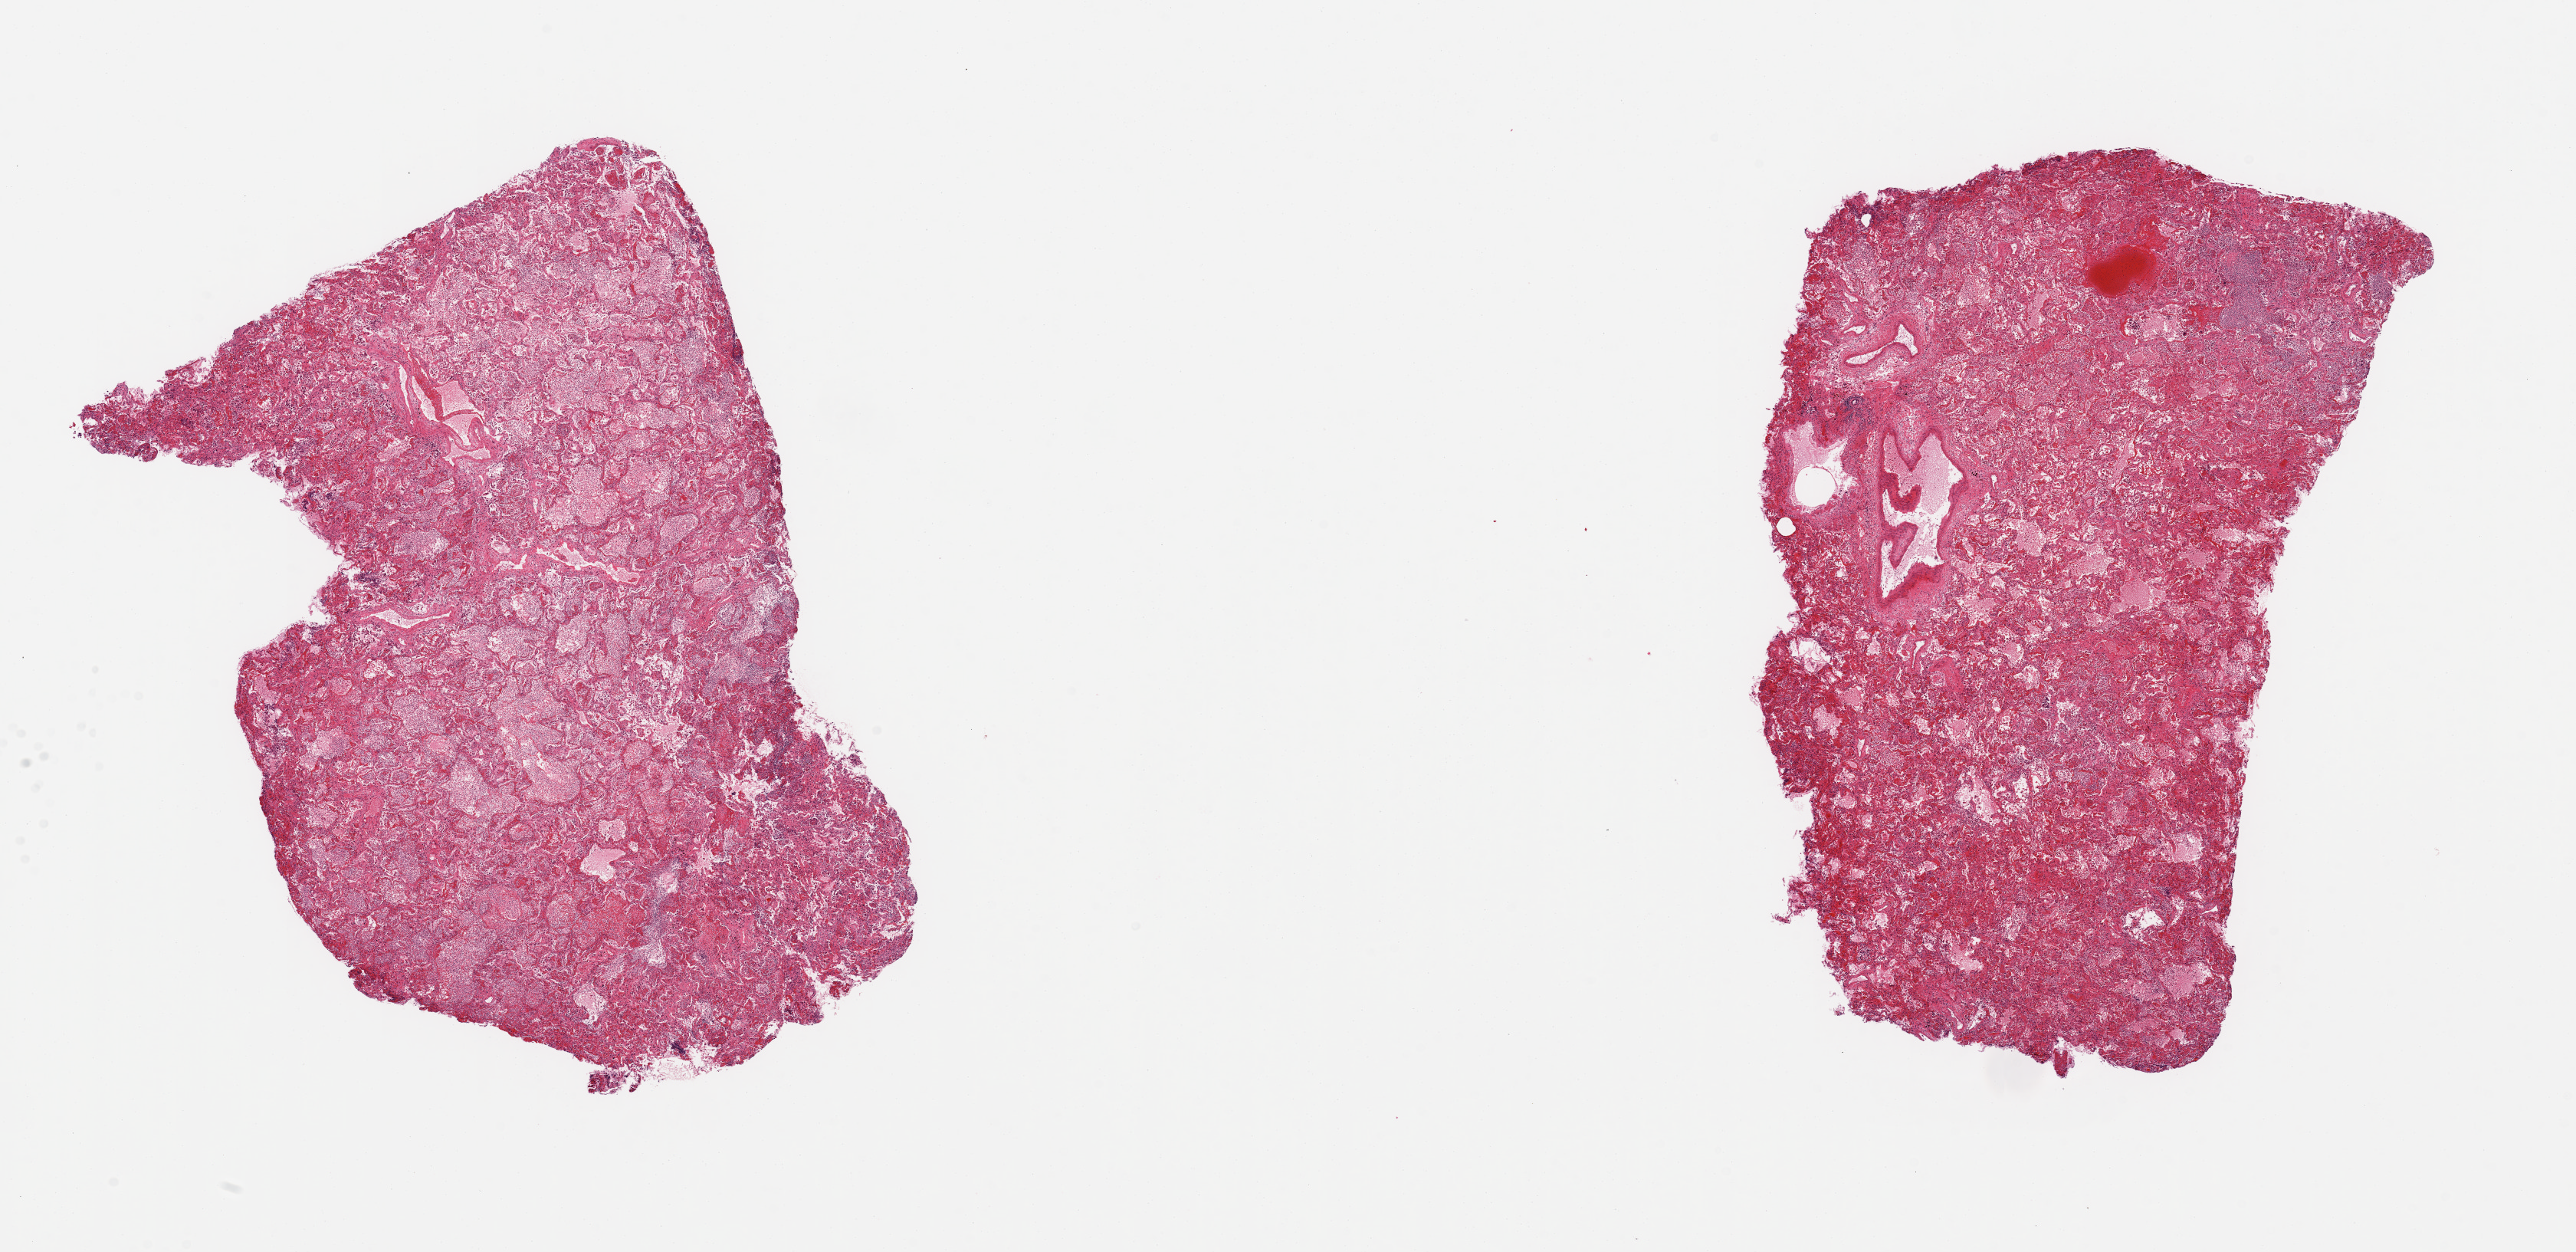
Whole-slide image, hematoxylin and eosin (H&E) stain, brightfield, shown as a low-resolution overview of the whole scanned area (about 26.6 x 12.9 mm, slide scanned at 20x). Male donor.
Specimen: PAXgene-fixed, paraffin-embedded tissue; section of lung (target tissue); donor tissue sample.